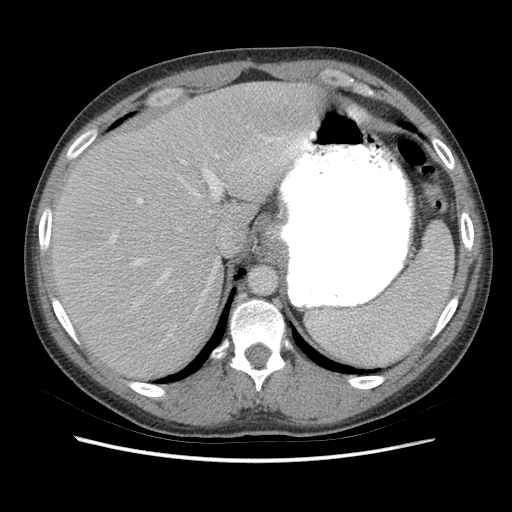
Contrast-enhanced abdominal CT (liver protocol), one axial slice; slice 52 of 73 in the series (ordered by position); reconstruction kernel STANDARD; 140 kVp; soft-tissue window (W 400 / L 40 HU); 512 × 512 image matrix, field of view 360 × 360 mm. From the clinical record (not read from this slice): diagnosis: hepatocellular carcinoma (patient treated with transarterial chemoembolisation; whether this scan precedes or follows treatment is not stated here); TNM stage (as recorded): Stage-IIIA; Child-Pugh class: A; tumour nodularity: multinodular.
Structures marked on this image (semi-automatic segmentation, software-assisted and operator-edited):
- liver parenchyma outside the tumour (the mass and vessels are separate outlines, so this box may not span the whole liver): bounding box <52,82,318,378> (left, top, right, bottom; pixels)
- liver vessels: <71,126,314,341>